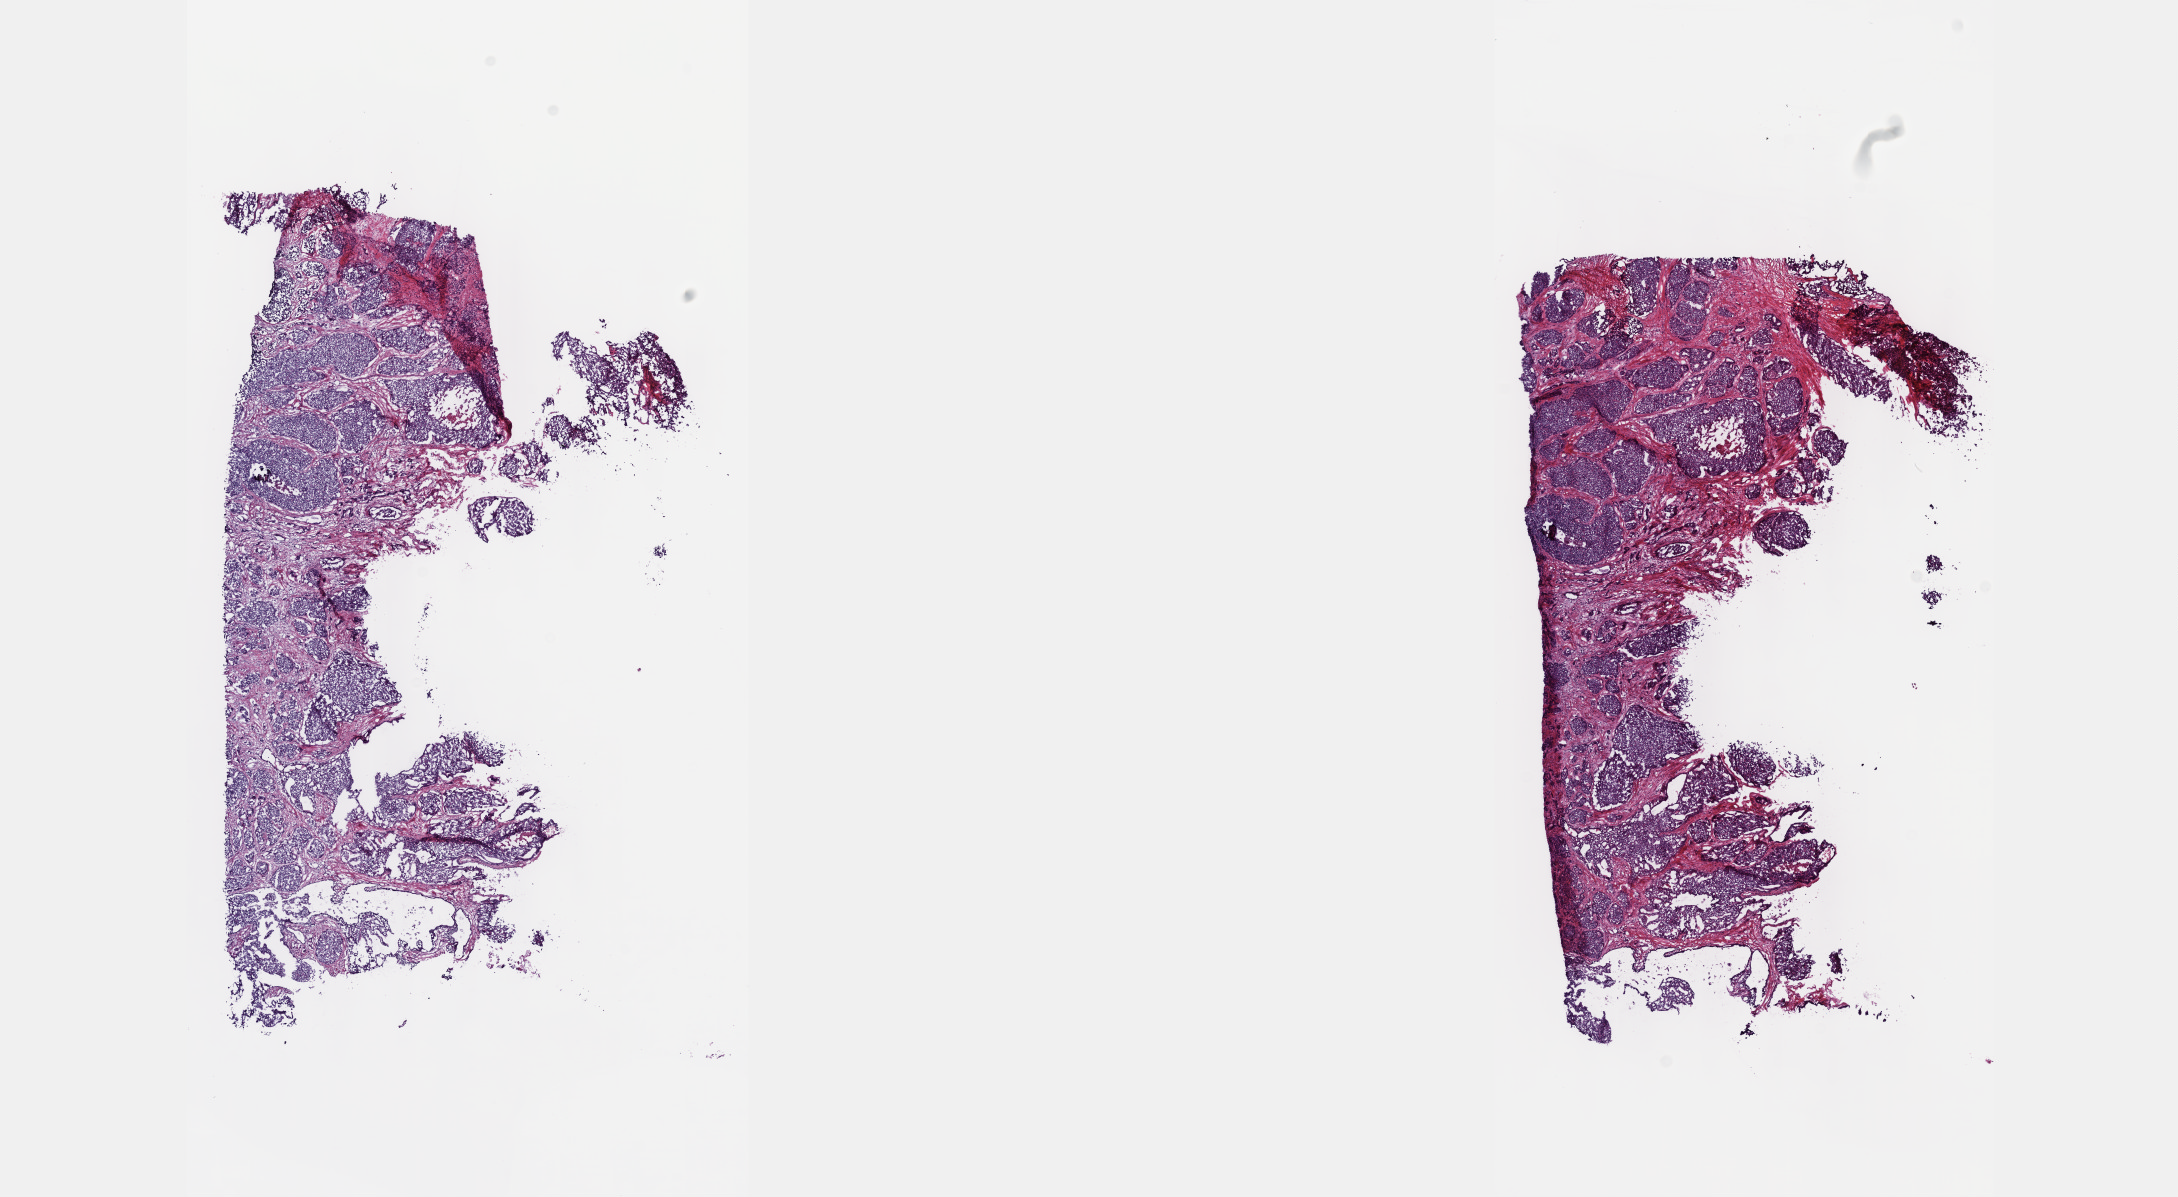
Hematoxylin and eosin (H&E) stained whole-slide image — whole scanned area (about 17.6 x 9.7 mm, acquisition: 40x scan) shown as a low-resolution overview, frozen section from the top of the tissue portion, sample: primary tumour, prostate. Male patient; age at initial diagnosis 59 years. Gleason score: 9 (4+5). Composition of this section per pathologist review: tumour cells 80%, tumour nuclei 80%, normal cells 0%, stromal cells 20%, necrosis 0%. Infiltration values recorded for this section: lymphocyte infiltration 40%, monocyte infiltration 20%, neutrophil infiltration 20%.
* pathologic diagnosis: Adenocarcinoma, NOS (prostate gland)
* laterality: bilateral
* lymph nodes positive (case pathology): 0 of 15 examined